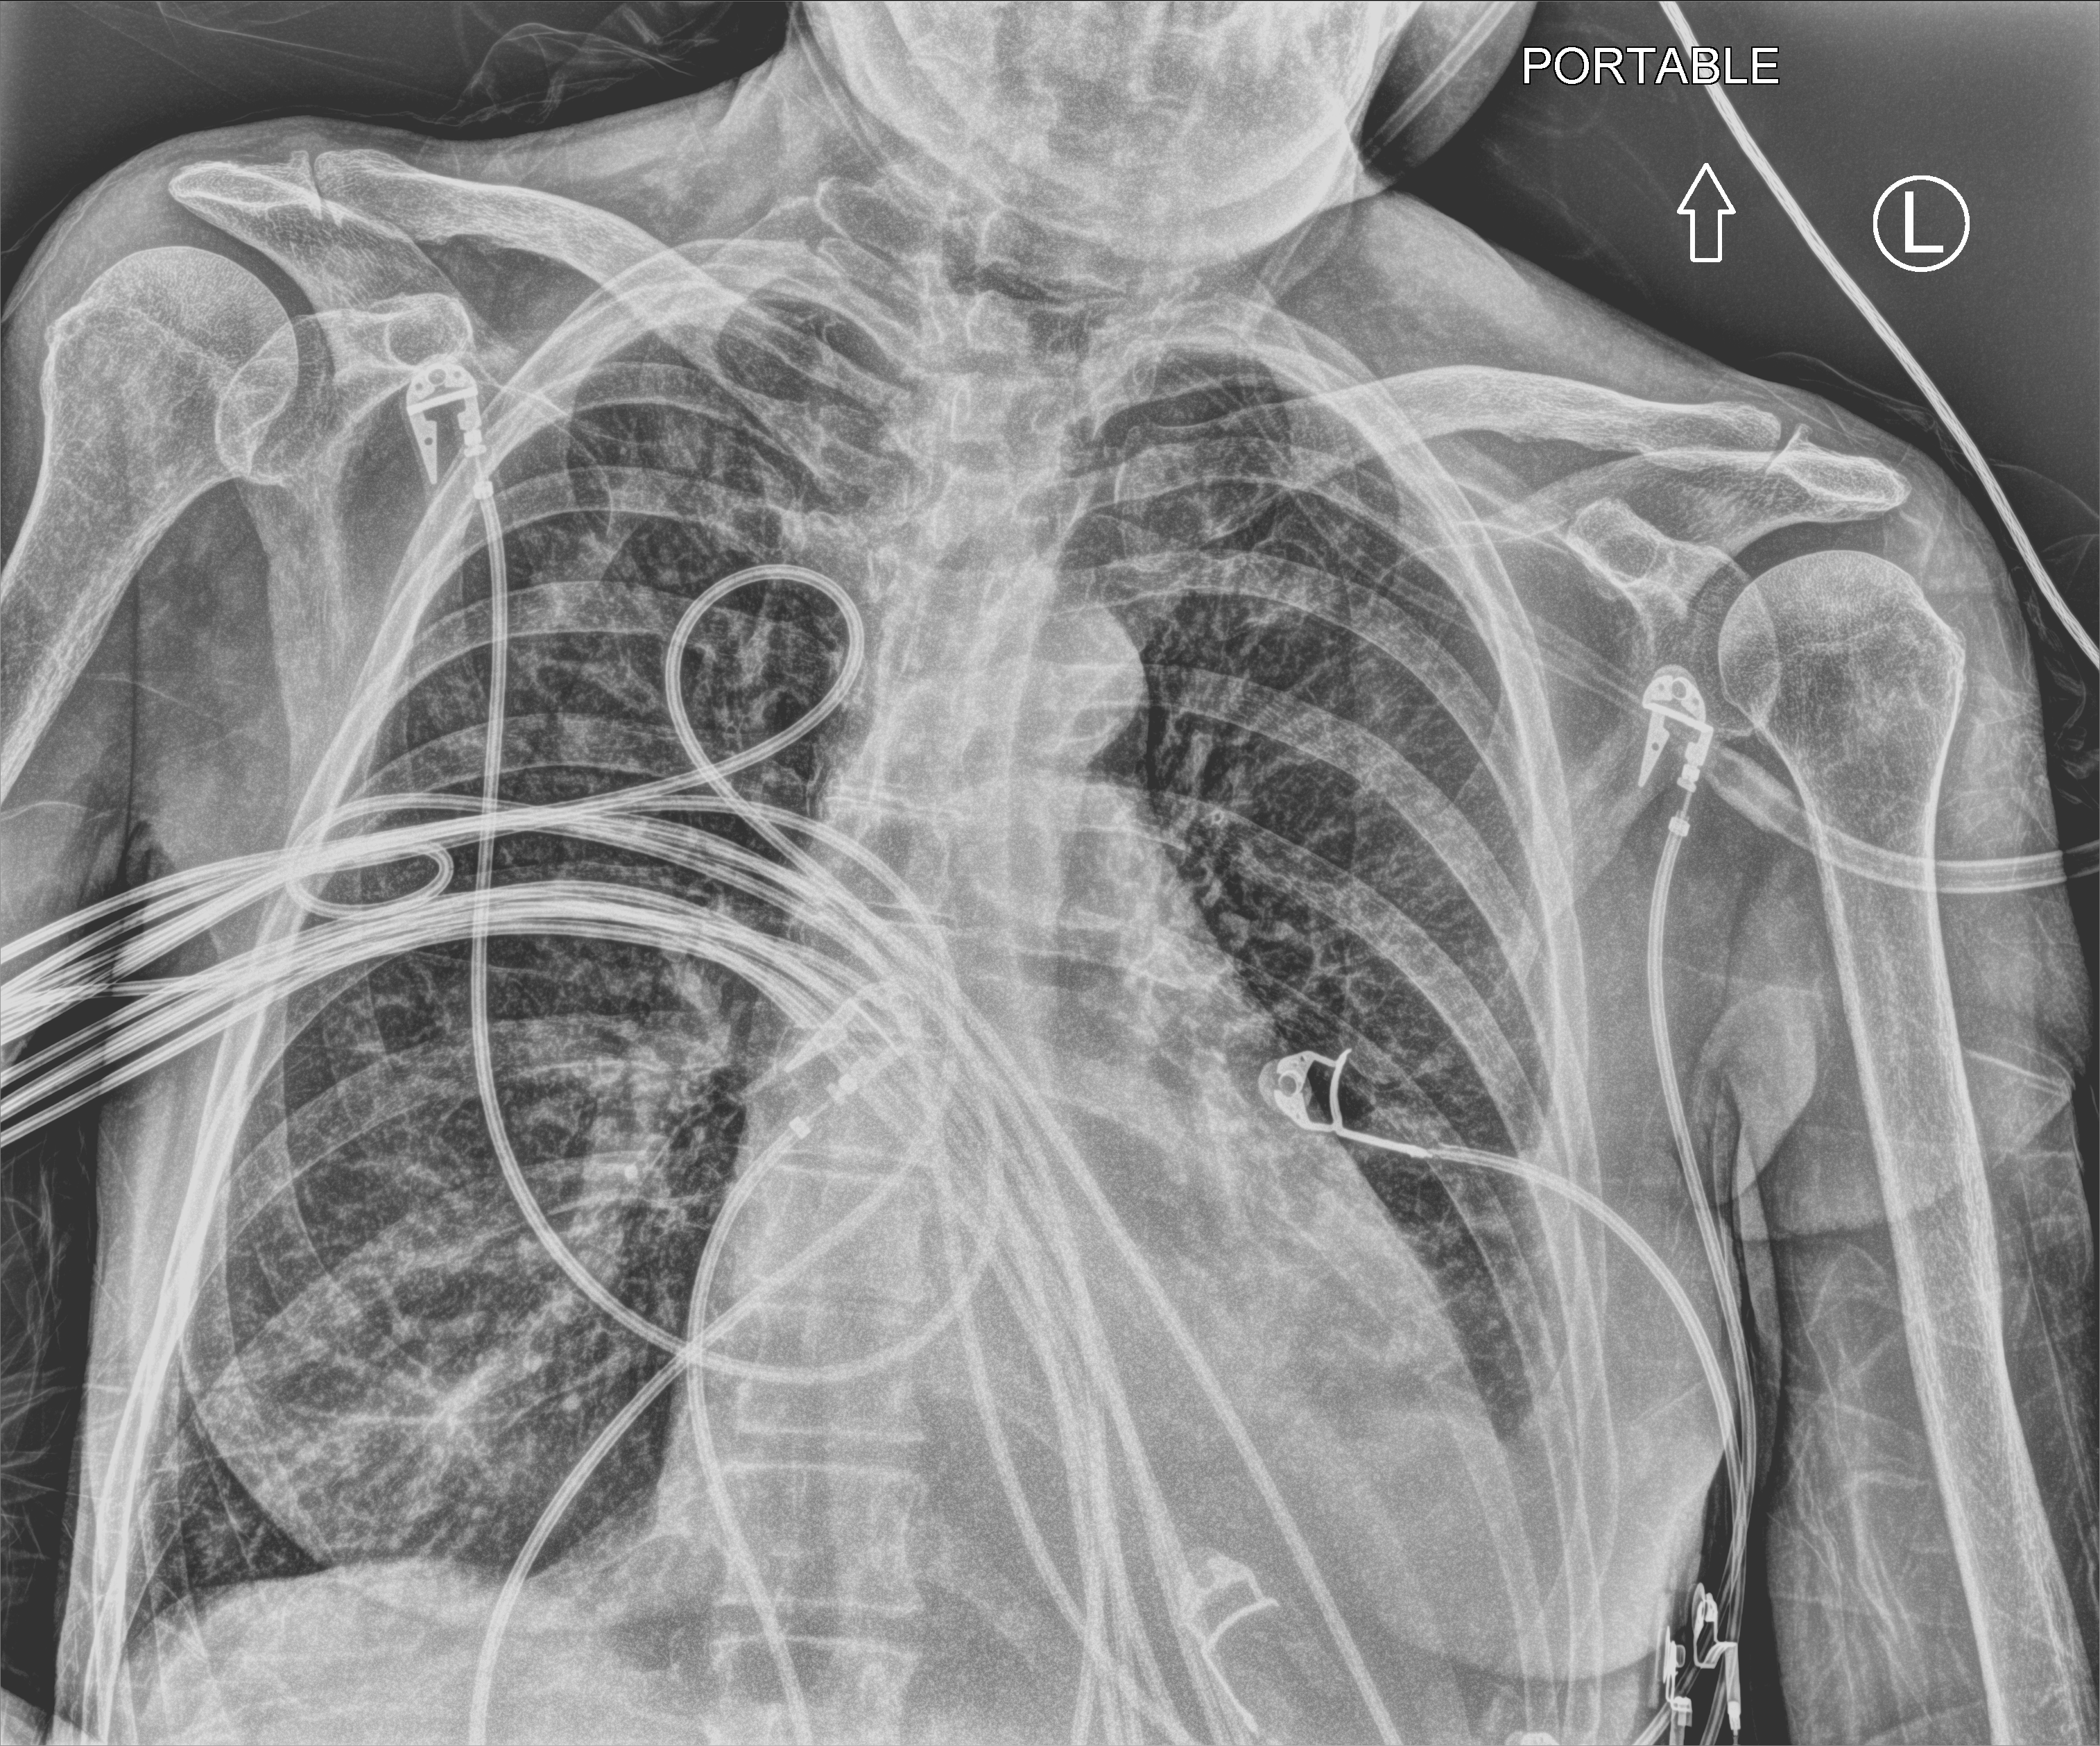
Portable chest radiograph, anteroposterior (AP) projection. Female patient hospitalised with COVID-19, age 60–74 years.
From the hospital-stay record, not from the radiograph (when in the stay this image was taken is not recorded):
- admitted to intensive care during this hospital stay: yes
- mechanically ventilated during this hospital stay: yes